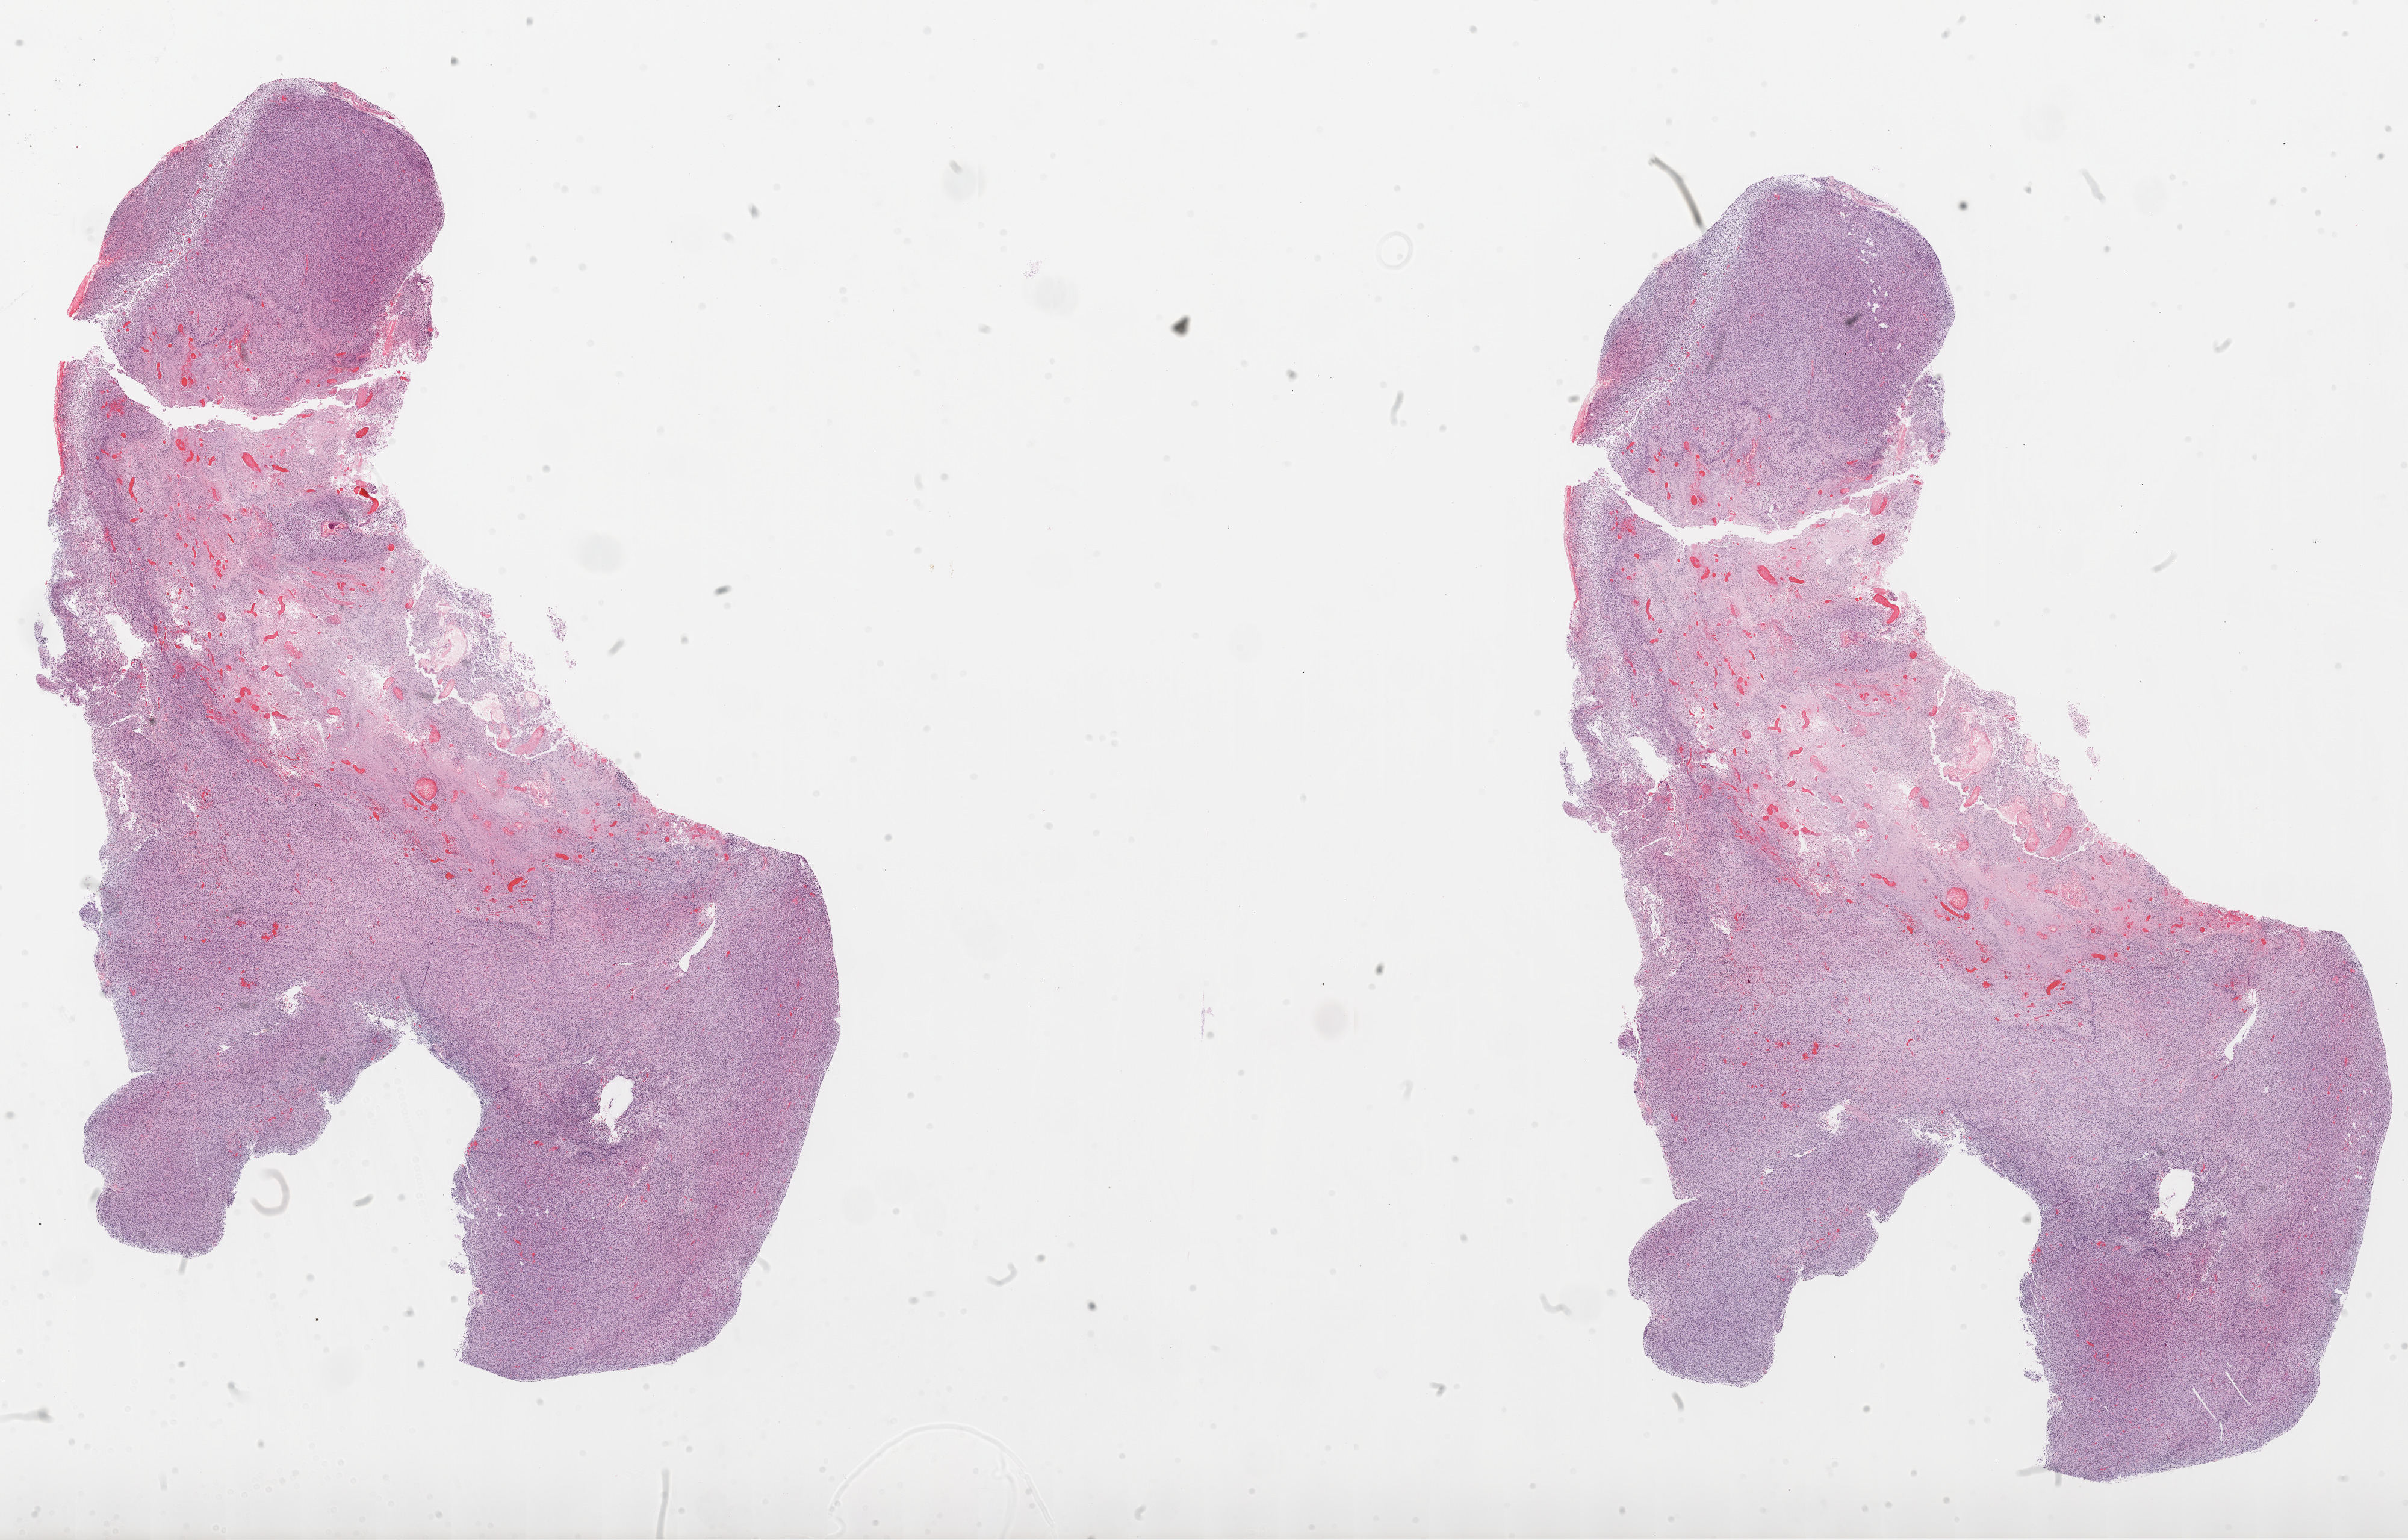
Digitized H&E tissue section (whole slide) — shown as a low-resolution overview of the whole scanned area (about 32.1 x 20.5 mm, slide scanned at 20x). Formalin-fixed paraffin-embedded (FFPE) diagnostic section. Sample: primary tumour, brain. Male, age 52 years at initial diagnosis.
* pathologic diagnosis: Glioblastoma